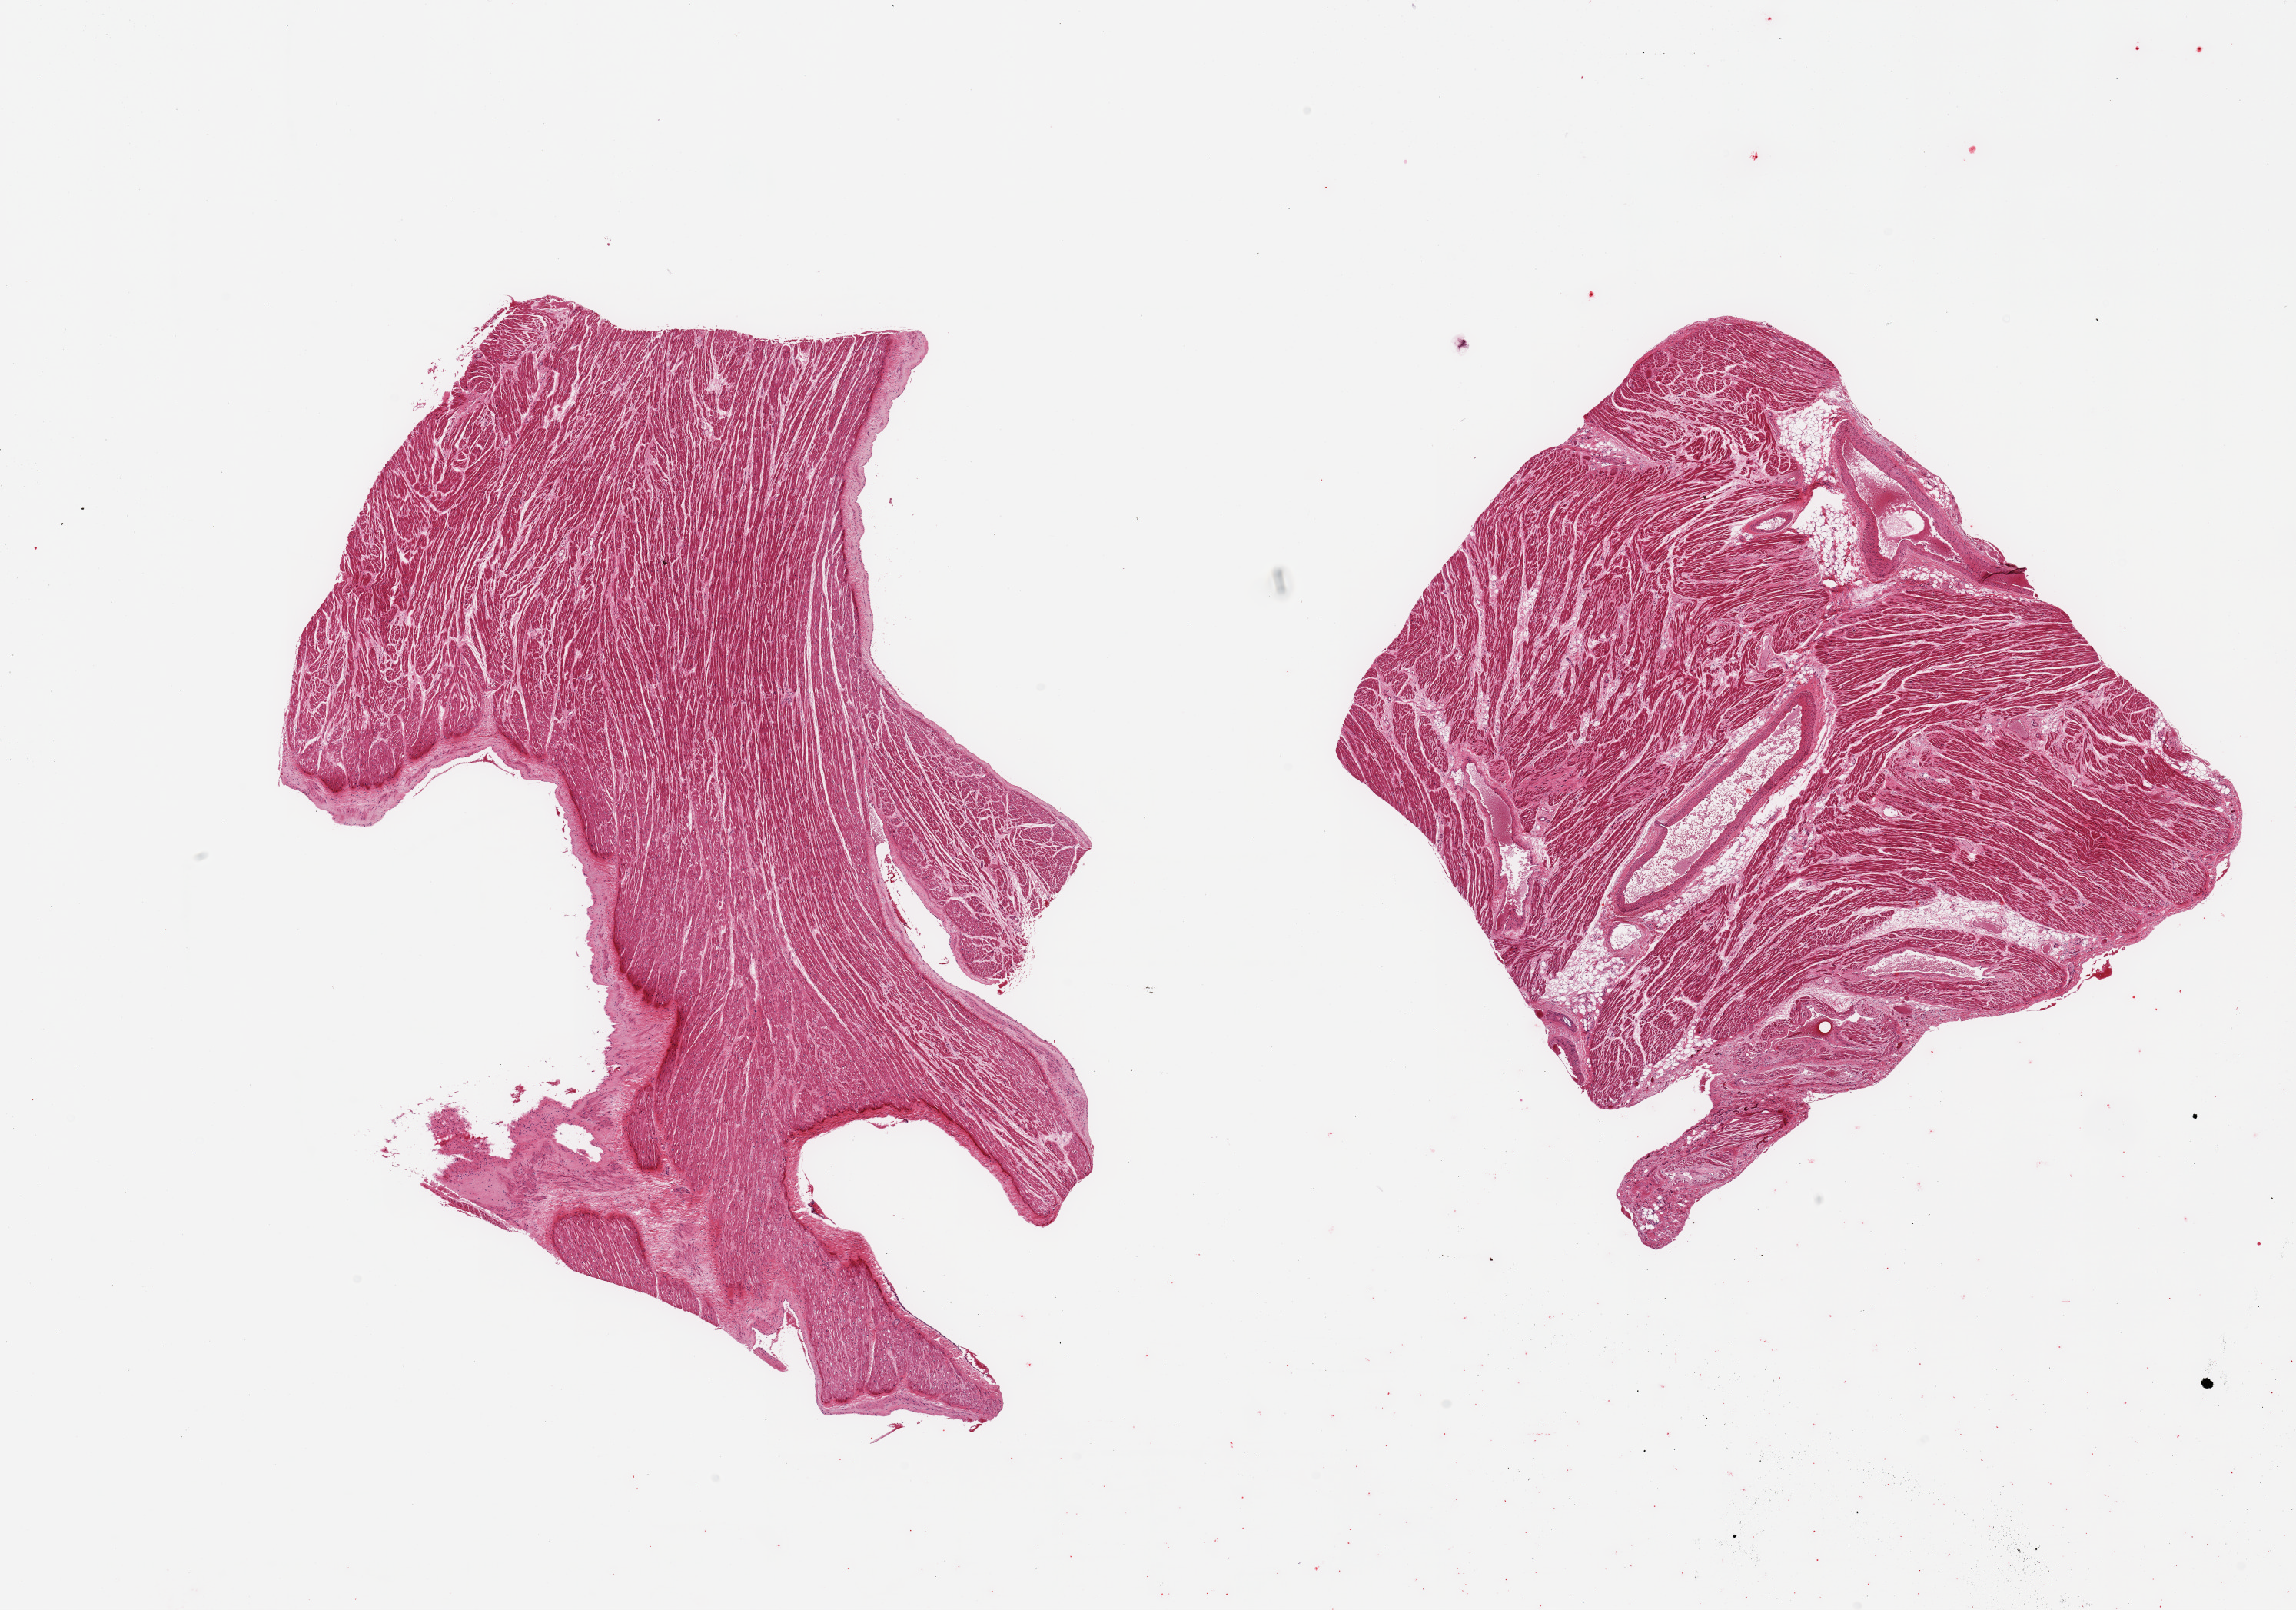
Digitized haematoxylin and eosin-stained section, shown as a low-resolution overview of the whole scanned area (about 23.6 x 16.6 mm, acquisition: 20x scan). PAXgene-fixed paraffin-embedded (PFPE) section. Section of auricular appendage (target tissue). Tissue donor sample. Donor sex: male.
Reviewer comment on this tissue sample: 2 pieces; less than 10% internal fat.